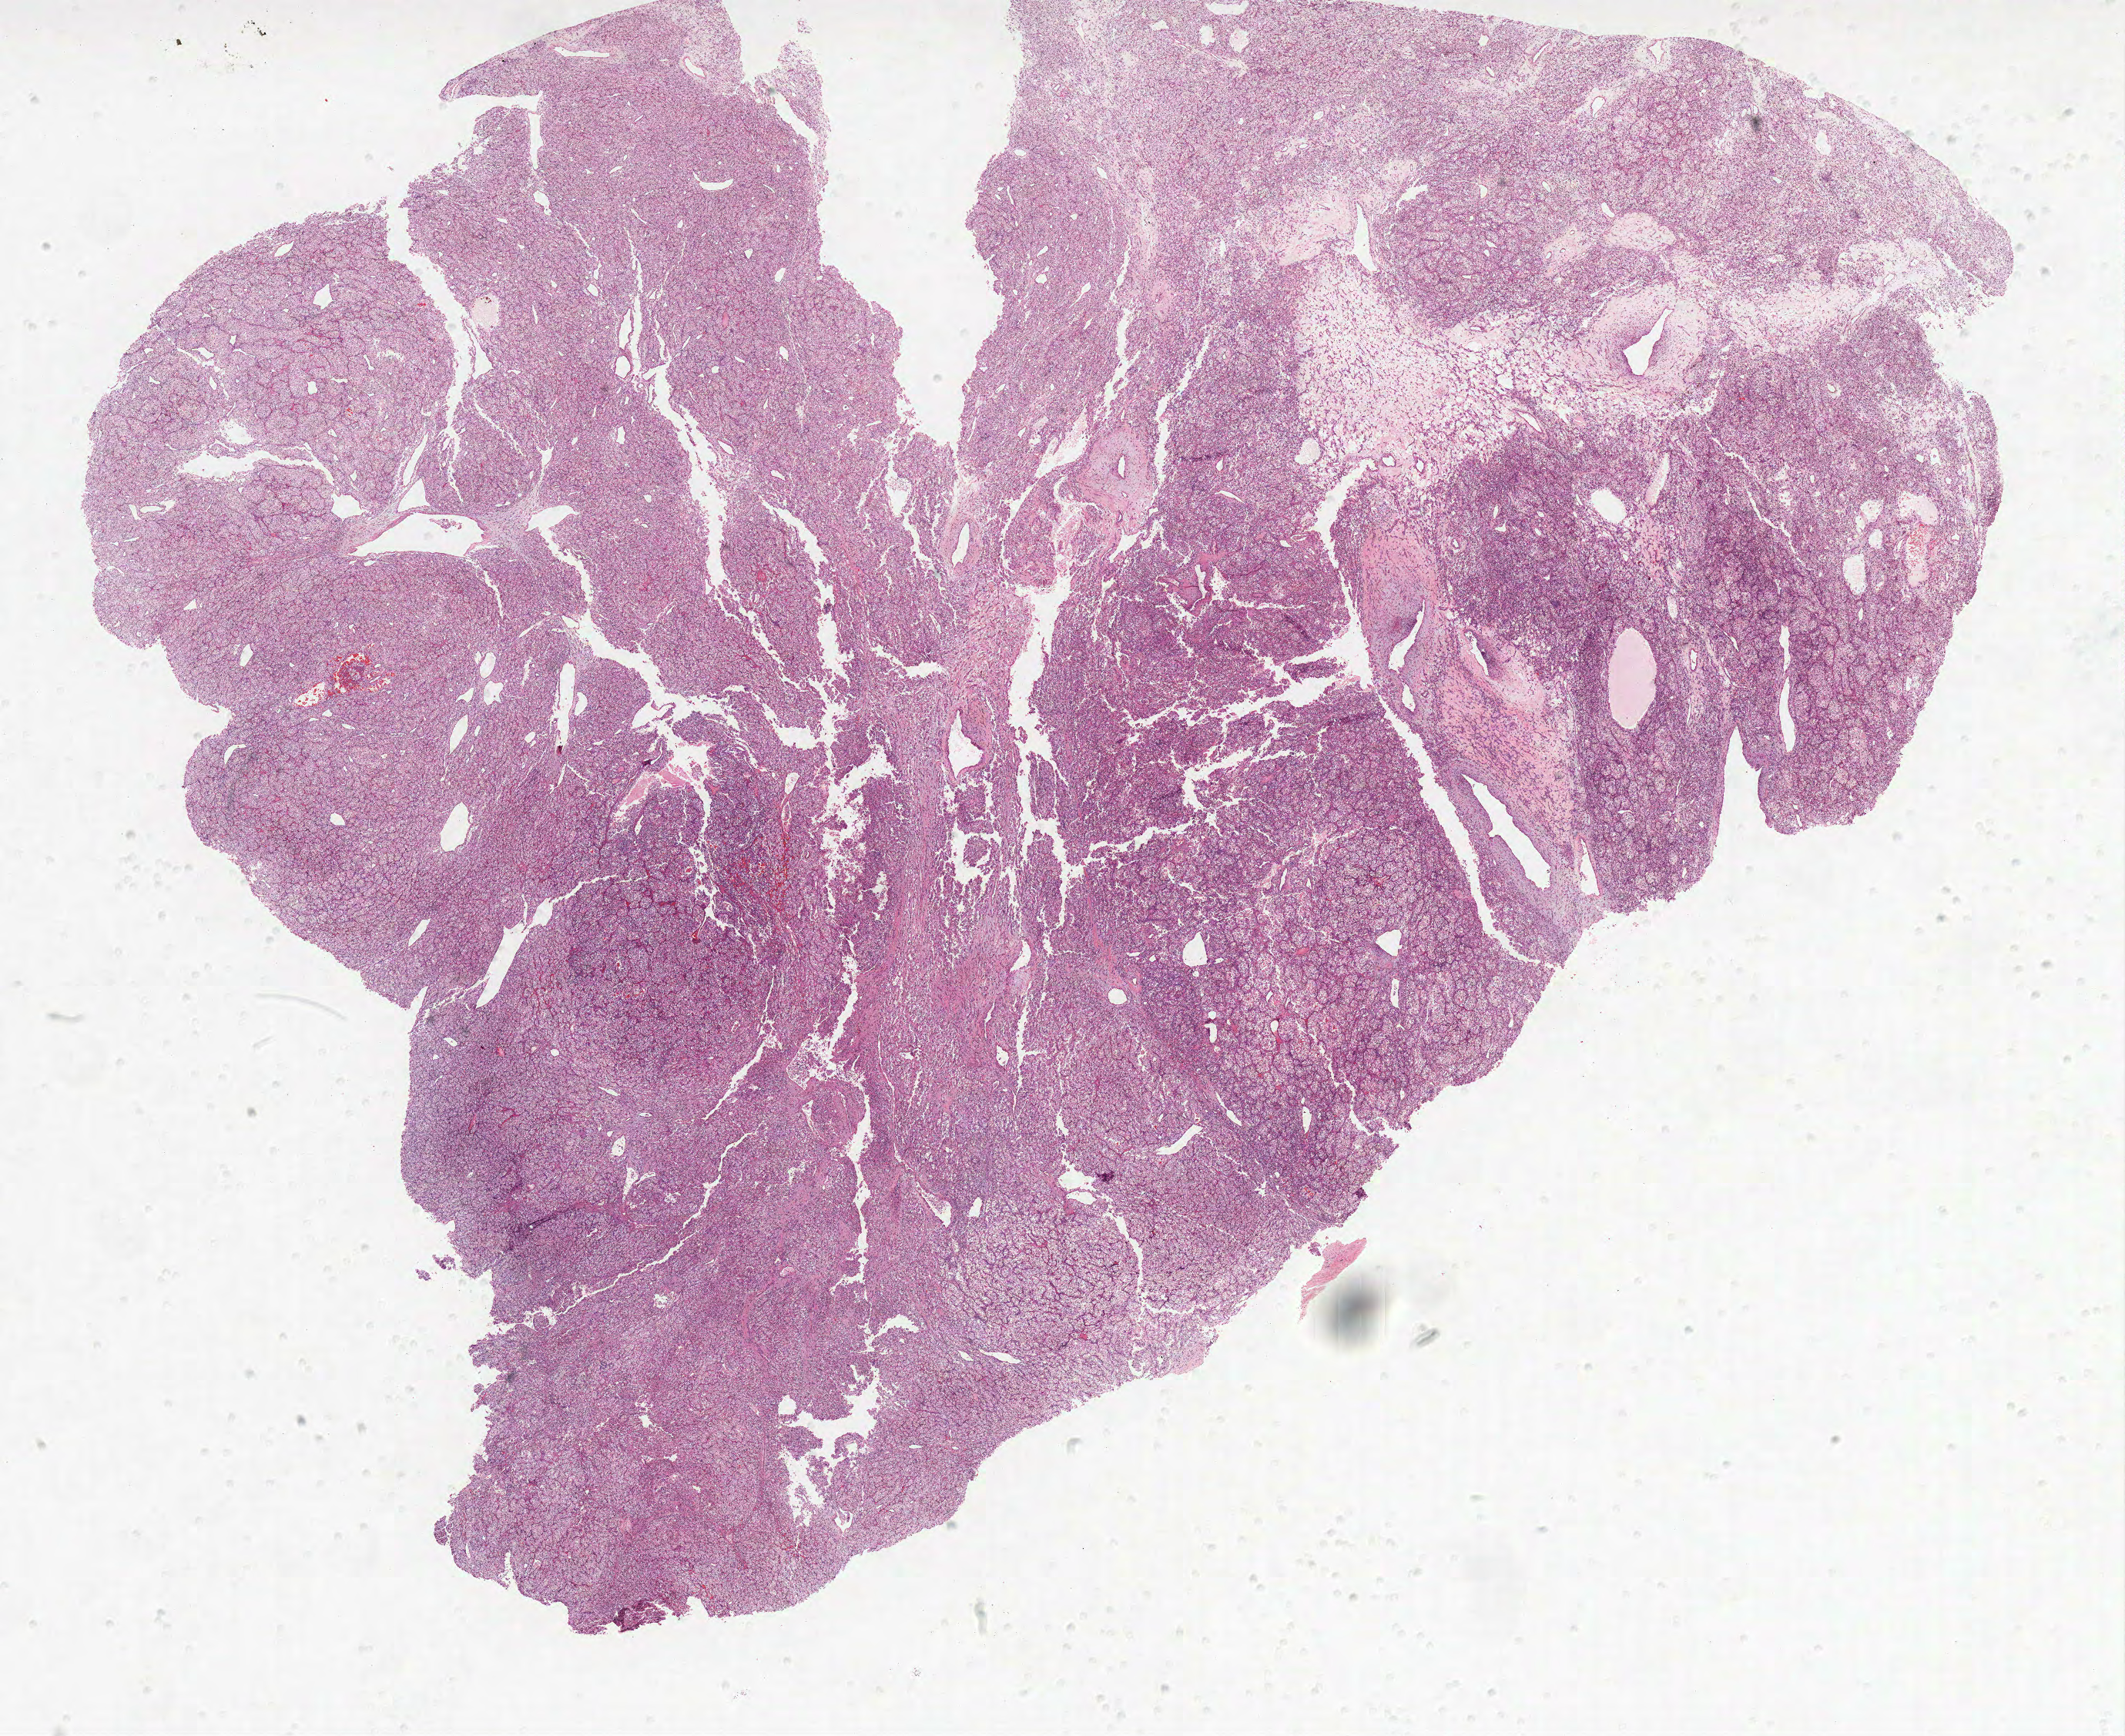
Digitized H&E-stained tissue section (whole slide), shown as a low-resolution overview of the whole scanned area (about 22.1 x 18.0 mm, from a 40x scan); FFPE section; kidney, primary tumour sample. Patient: male, age at initial diagnosis 50 years. Histologic grade: G2 (moderately differentiated).
Diagnosis: Clear cell adenocarcinoma, NOS. AJCC pathologic stage: I.